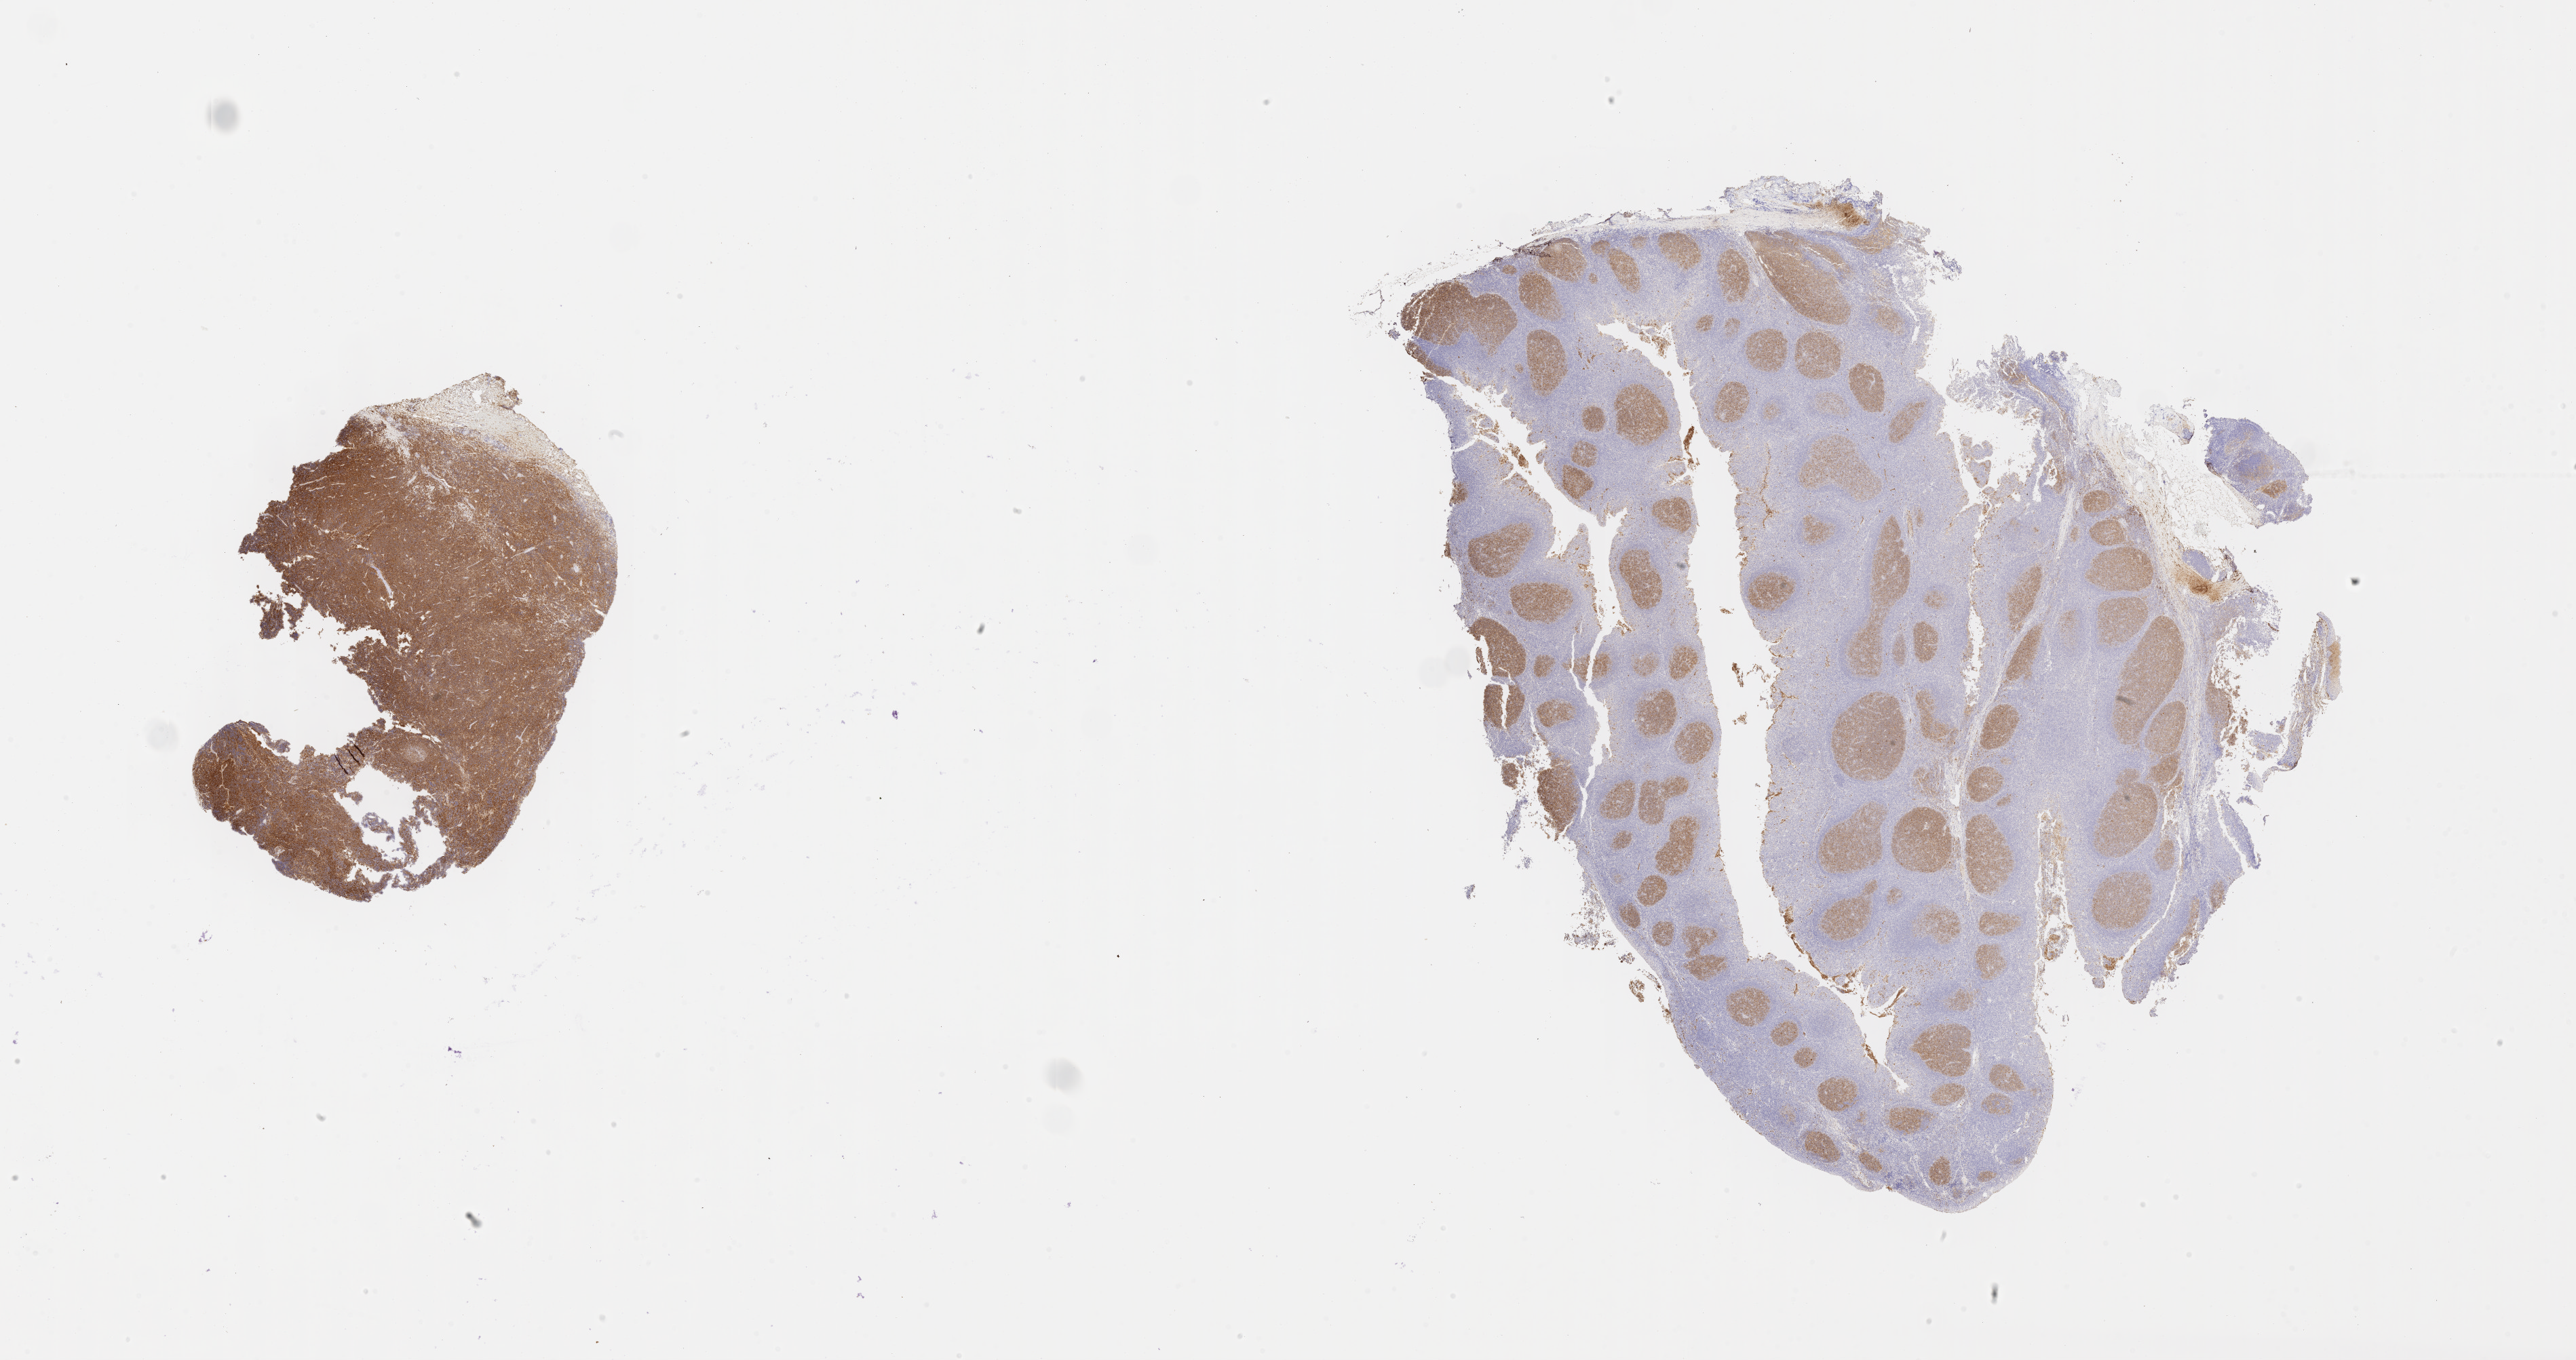
IHC for CD10, whole-slide image — whole scanned area (about 30.7 x 16.2 mm) shown as a low-resolution overview. Tumor tissue. Site: mandible. Patient: female, age at initial diagnosis 7 years.
* diagnosis: Burkitt lymphoma, NOS